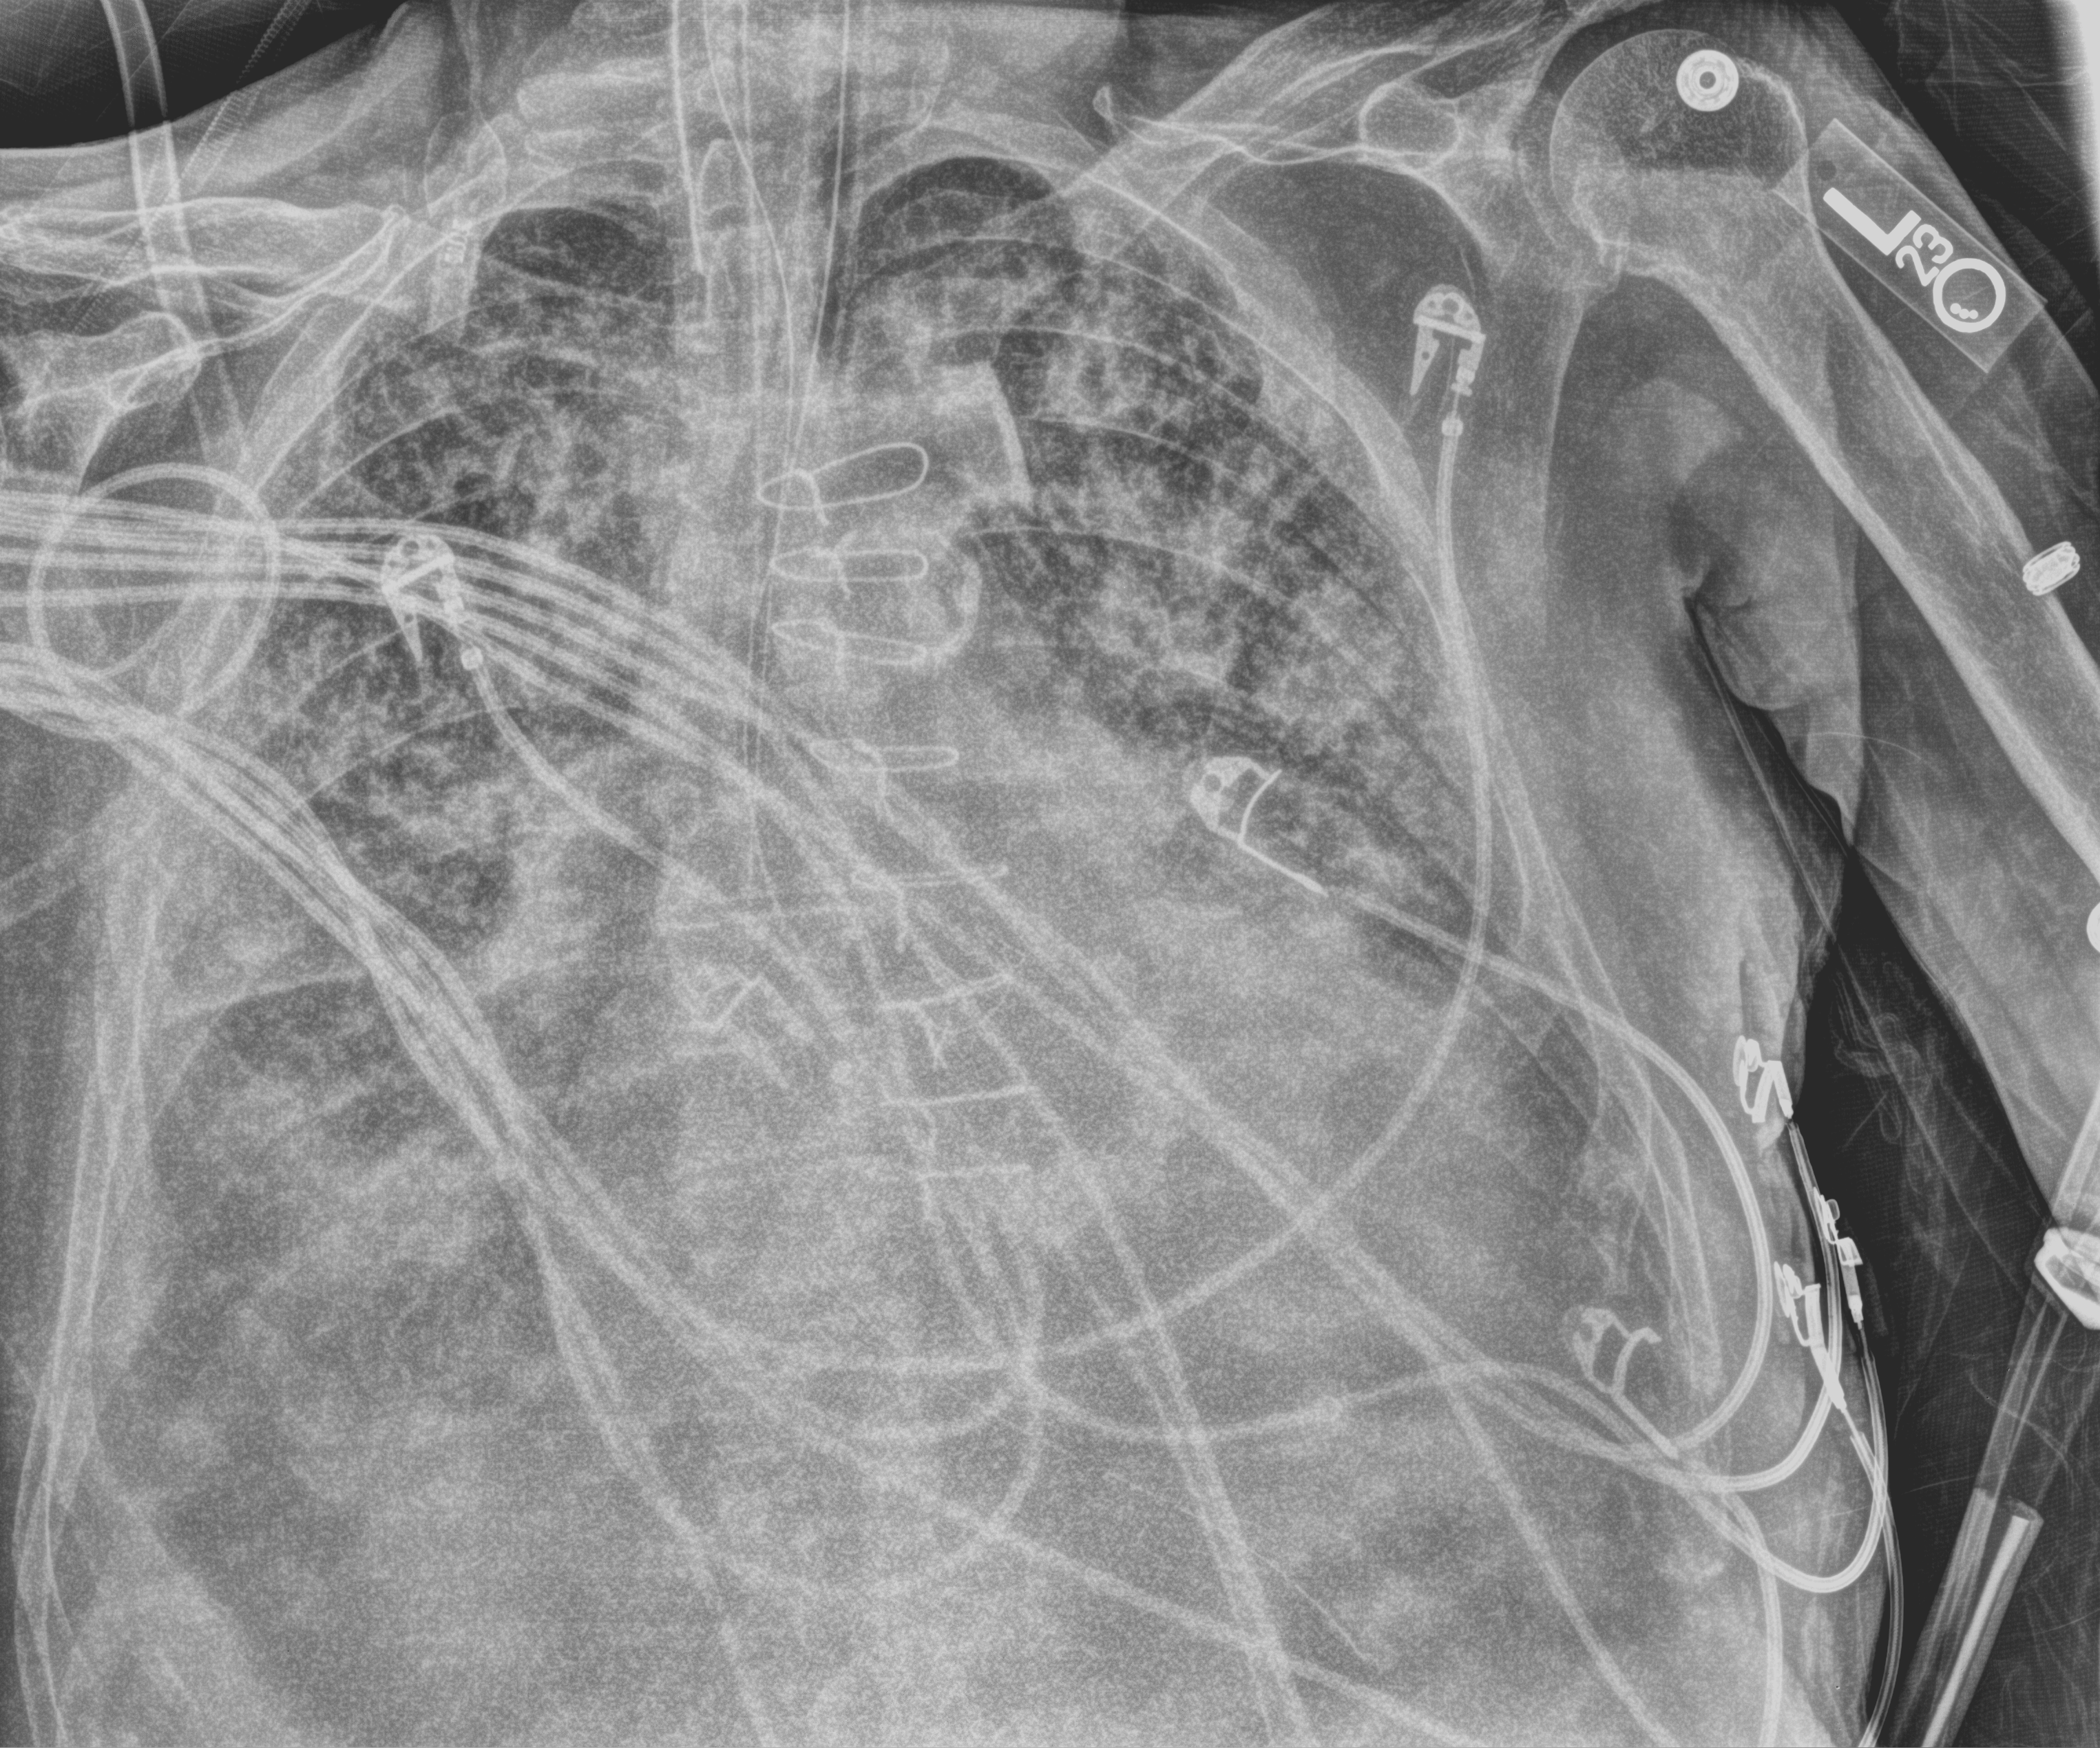
Bedside chest radiograph (computed radiography); anteroposterior (AP) projection. Male patient hospitalised with COVID-19, age 75–90 years.
Hospital-stay facts (about this admission, not read from this image; timing relative to this image not recorded):
- length of hospital stay: 40 days